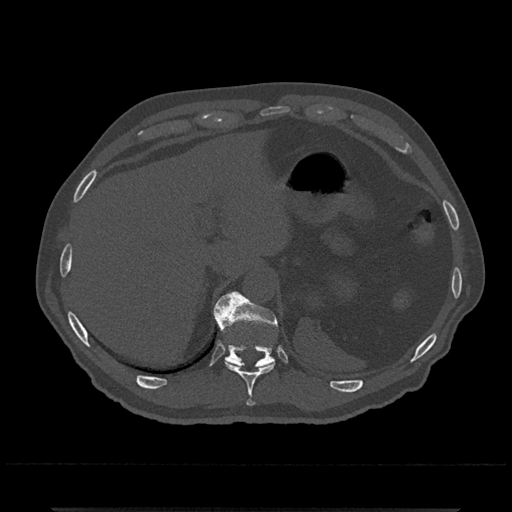
CT including the spine, one axial slice; slice 527 of 797 in the series (ordered by position); reconstruction kernel Br40s/3; 120 kVp; bone window (W 1800 / L 400 HU); 0.5 mm slice thickness; 512 × 512 image matrix. Patient: male, 67 years. Case-level facts recorded for this patient, not image findings: primary cancer: prostate.
Annotated regions visible in this slice (semi-automatically segmented with operator editing):
- T10 vertebra: bounding box <219,325,275,407> (left, top, right, bottom; pixels)
- T11 vertebra: <213,292,278,367>